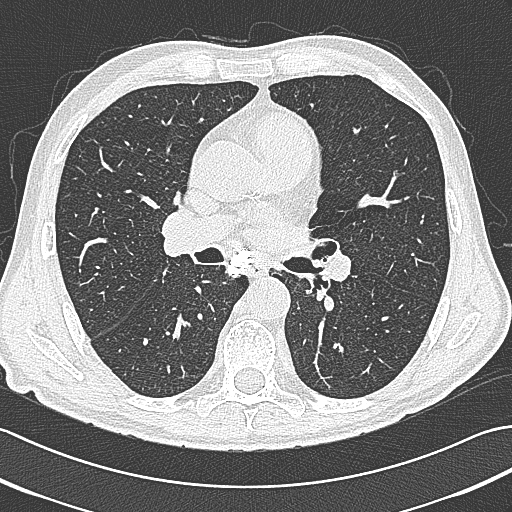
Axial slice from a low-dose chest CT screening exam; first (baseline) screen; lung window (W 1500 / L -600 HU); lung (sharp) reconstruction kernel (B80f); slice 174 of 380 in the series. Male participant, aged 65 years at enrolment.
Lesion marked by an expert reader, bounding box <303,229,346,278> (left, top, right, bottom; pixels). Screening reader's record for this exam: no non-calcified nodule ≥4 mm recorded. Official screen result: negative screen, minor abnormalities not suspicious for lung cancer. Later outcome: lung cancer diagnosed 161 days after this screen — large cell neuroendocrine carcinoma, left hilum, left main stem bronchus, stage IIIB (AJCC 6th edition), 70 mm at pathology.